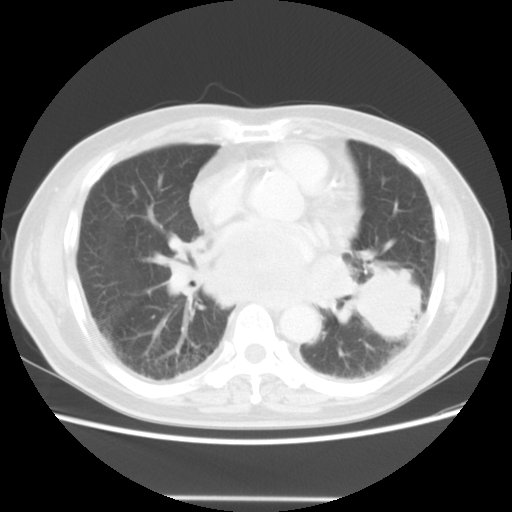
Chest CT, one axial slice; lung window (W 1500 / L -600 HU); 512 × 512 image matrix. Patient: male, 66 years. From the clinical record (not read from this slice): clinical TNM (as recorded): T4 N3 M0; histopathological grade: G3.
Structures marked on this image (rectangle marked by the reading radiologist):
- lung tumour (recorded histology: small cell carcinoma): bounding box [x1, y1, x2, y2] px = [347, 271, 433, 344]